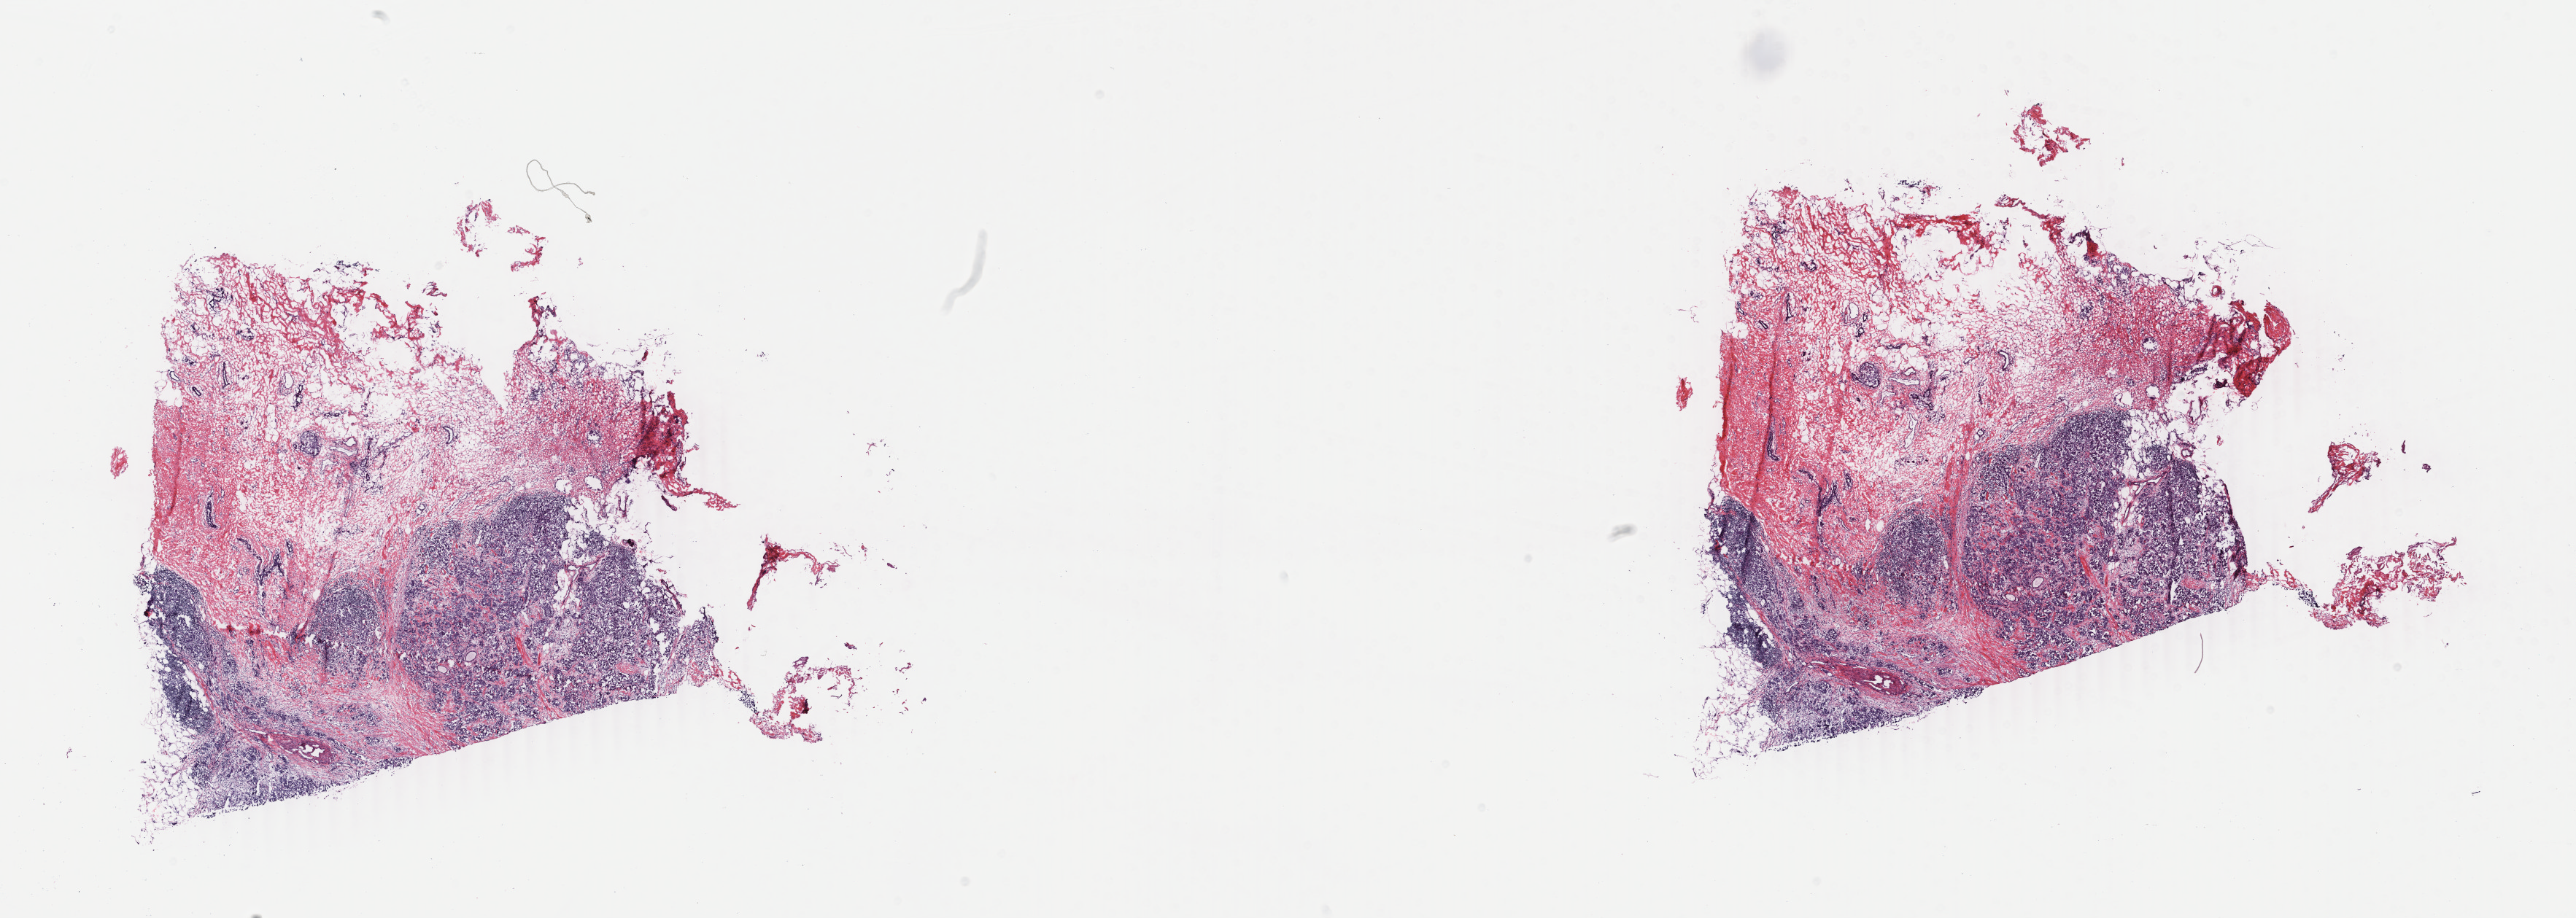
Digitized H&E tissue section (whole slide) — low-resolution overview of the scanned area, about 28.1 x 10.0 mm (from a 40x scan). Frozen section. Primary tumour sample from the breast. Female, age 49 years at initial diagnosis. Slide review estimates, as recorded: tumour cells 70%, tumour nuclei 70%, normal cells 5%, stromal cells 25%, necrosis 0%. Infiltration values recorded for this section: lymphocyte infiltration 2%, monocyte infiltration 0%, neutrophil infiltration 0%.
AJCC pathologic stage: IIIA. TNM: T2 N2a M0. Pathologic diagnosis: Infiltrating duct mixed with other types of carcinoma.